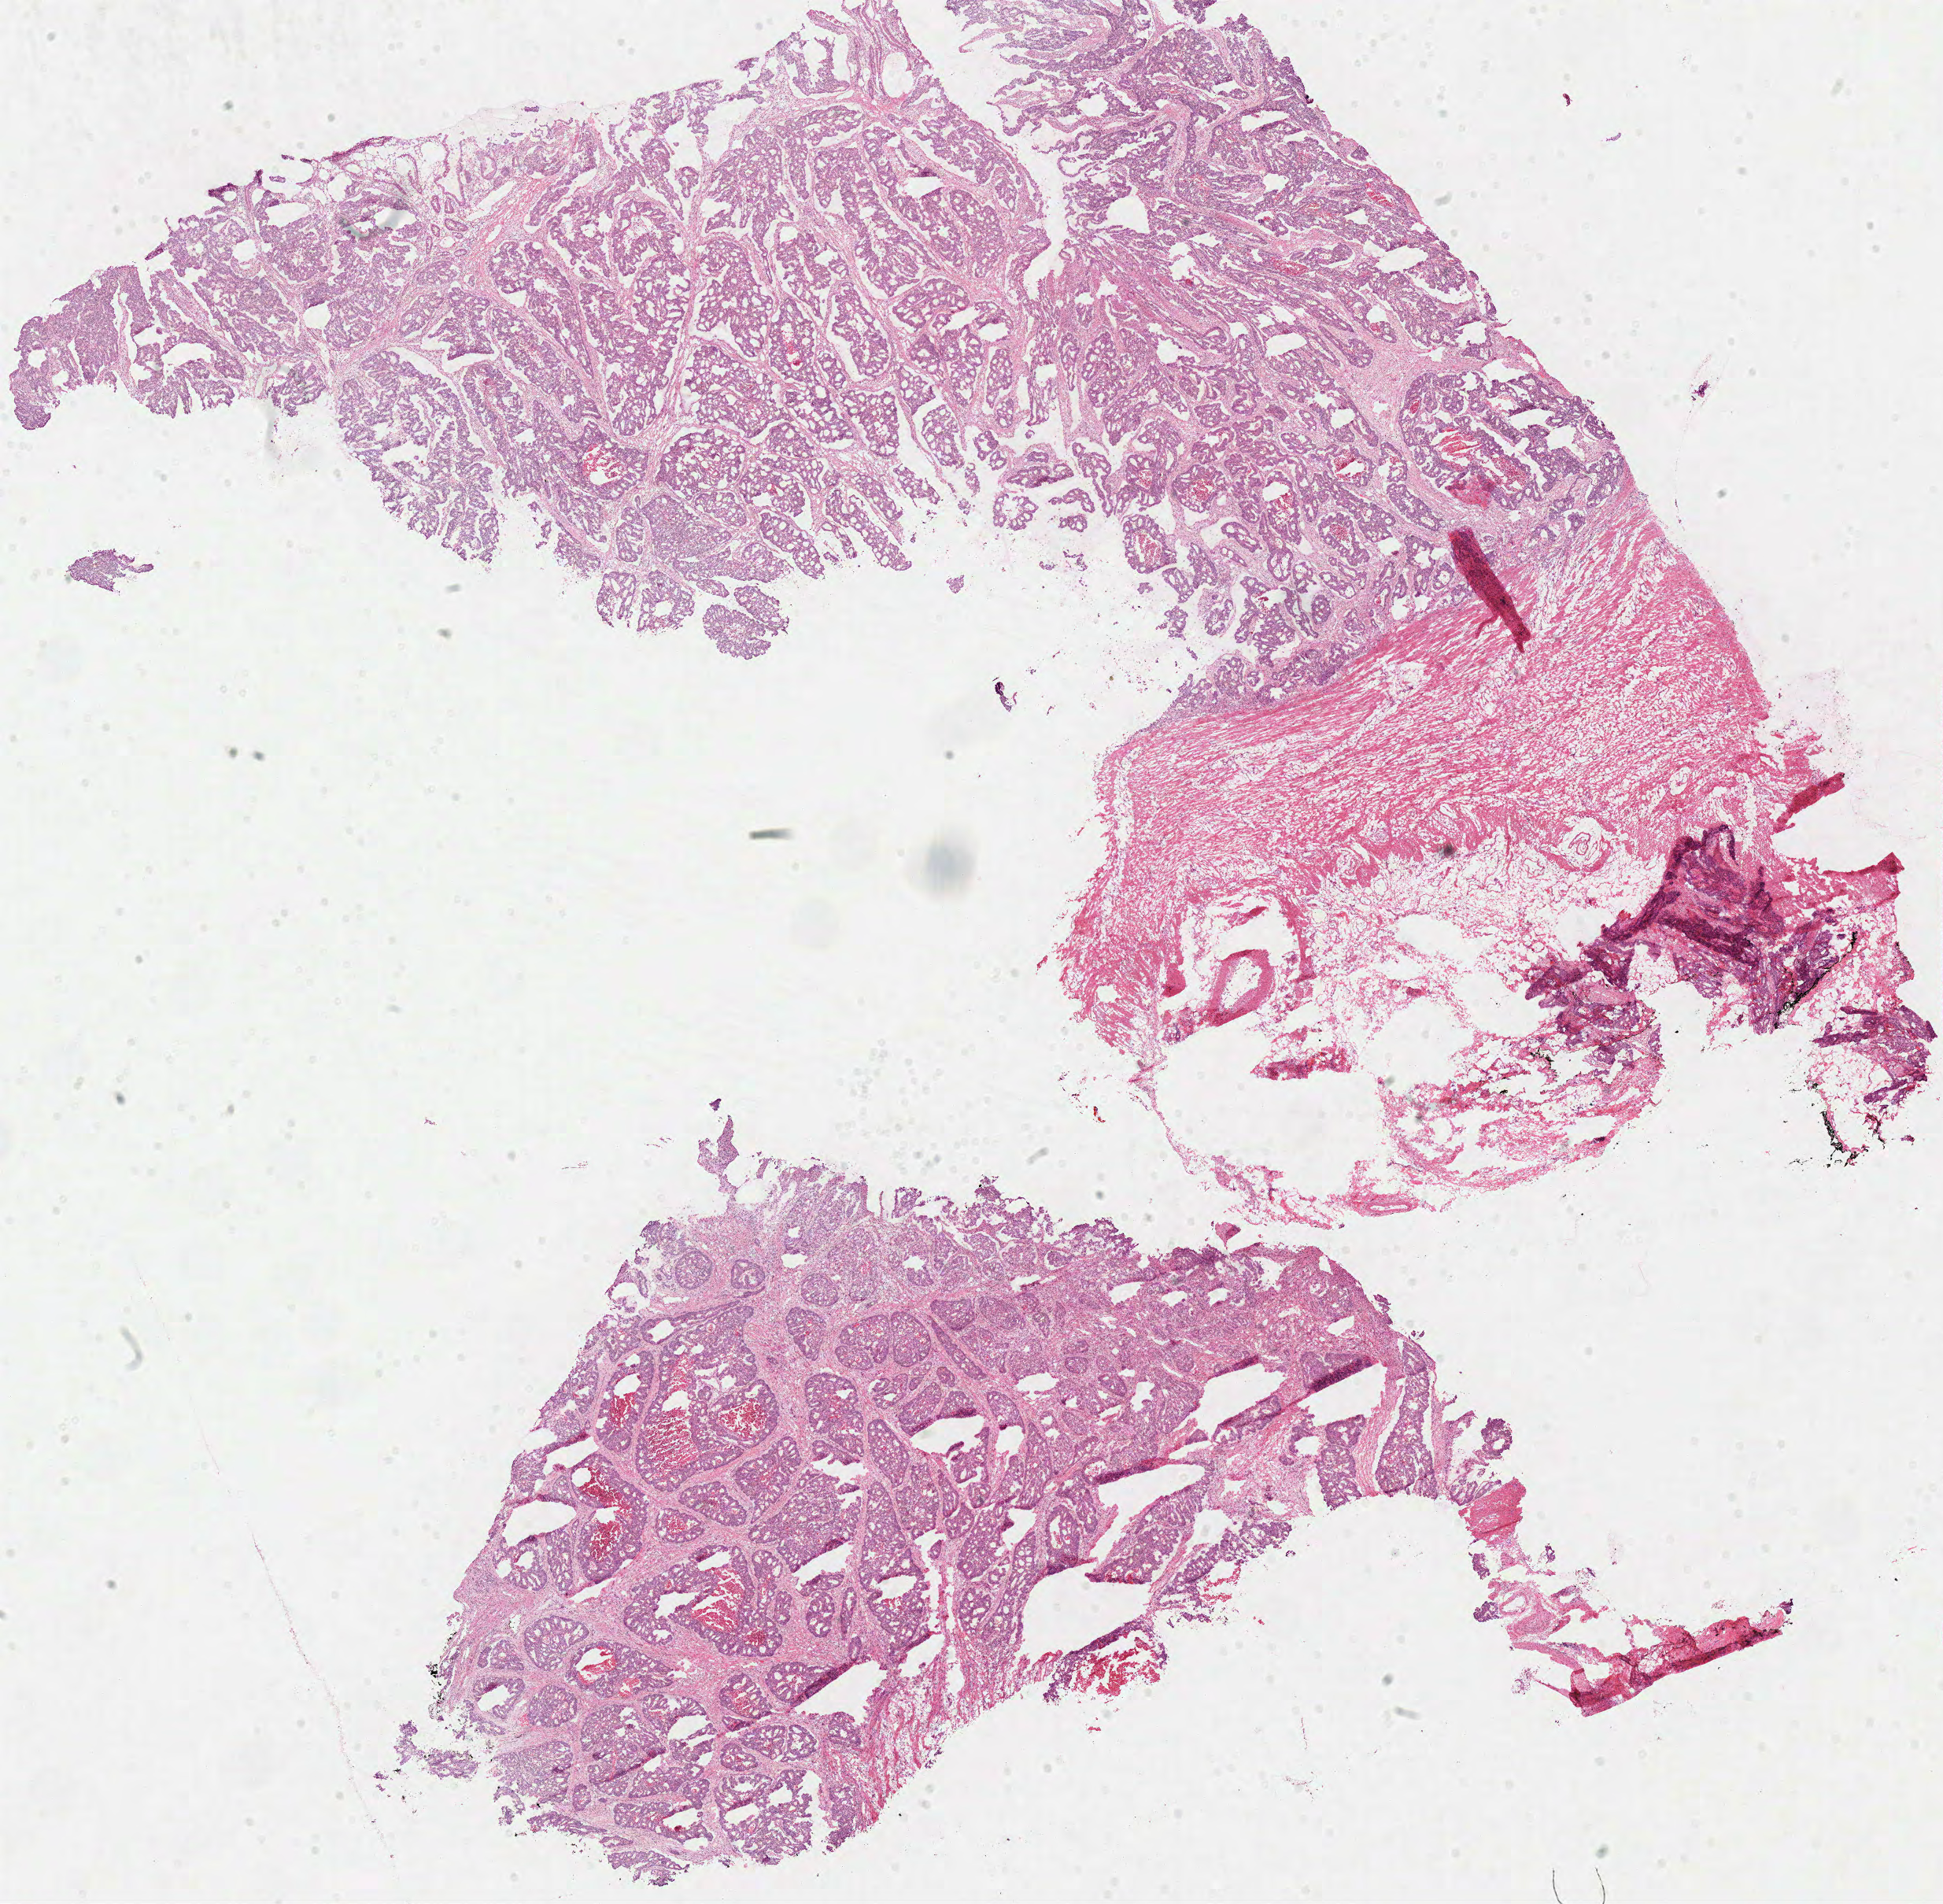
H&E whole-slide image — shown as a low-resolution overview of the whole scanned area (about 19.5 x 19.1 mm), frozen section from the top of the tissue portion, colon, primary tumour sample. Female, age 48 years at initial diagnosis. Slide review estimates, as recorded: tumour cells 77%, tumour nuclei 85%, normal cells 0%, stromal cells 15%, necrosis 8%.
* diagnosis: Adenocarcinoma, NOS (ascending colon)
* lymph nodes positive (case pathology): 0 of 33 examined
* AJCC pathologic stage: I